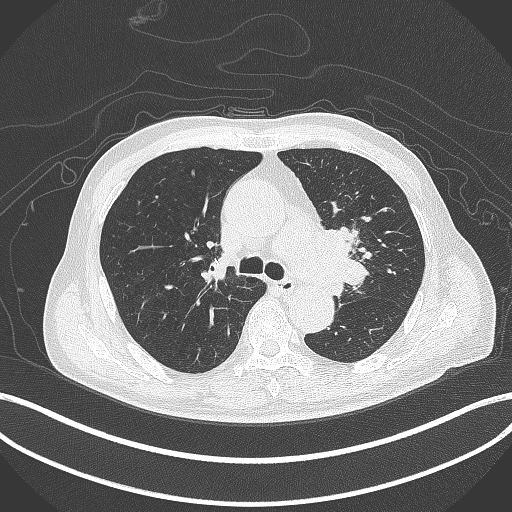
Chest CT, one axial slice. Slice 283 of 417 in the series (ordered by position). Reconstruction kernel B70f. Lung window (W 1500 / L -600 HU). 1 mm slice thickness. 512 × 512 image matrix, field of view 400 × 400 mm. Male patient, age 77 years. Case-level facts recorded for this patient, not image findings: clinical TNM (as recorded): T3 N1 M0.
Structures marked on this image (bounding box drawn by a radiologist):
- lung tumour (recorded histology: adenocarcinoma): box from (x=314, y=221) to (x=368, y=299) px